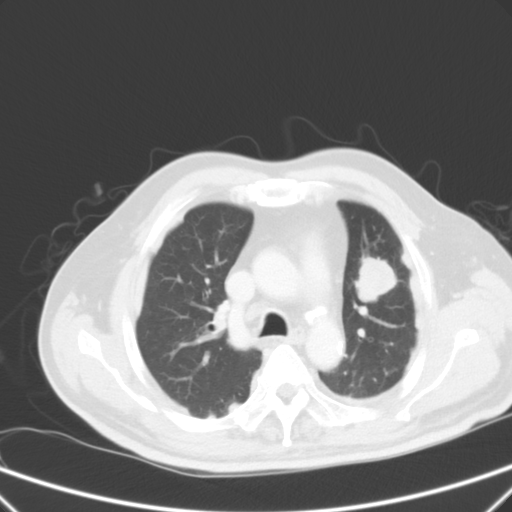
Chest CT, one axial slice. Intravenous contrast given. Lung window (W 1500 / L -600 HU). 5 mm slice thickness. 512 × 512 image matrix, field of view 357 × 357 mm. Male patient, age 66 years. From the clinical record (not read from this slice): clinical TNM (as recorded): T1c N3 M1a.
Annotated regions visible in this slice (bounding box drawn by a radiologist):
- lung tumour (recorded histology: squamous cell carcinoma): box from (x=355, y=253) to (x=401, y=311) px